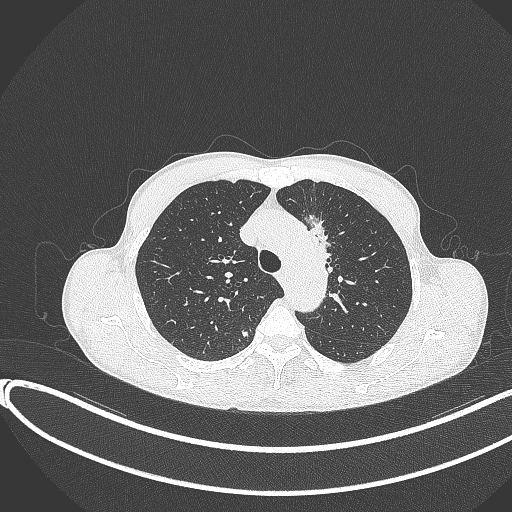
Chest CT, one axial slice. Position 282 of 374 along the scan axis. Reconstruction kernel B70f. Lung window (W 1500 / L -600 HU). 1 mm slice thickness. 512 × 512 image matrix, field of view 400 × 400 mm. Patient: male, 58 years. From the clinical record (not read from this slice): clinical TNM (as recorded): T1c N1 M0.
Structures marked on this image (rectangle marked by the reading radiologist):
- lung tumour (recorded histology: adenocarcinoma): bounding box (x1, y1, x2, y2) in pixels: (299, 212, 336, 270)